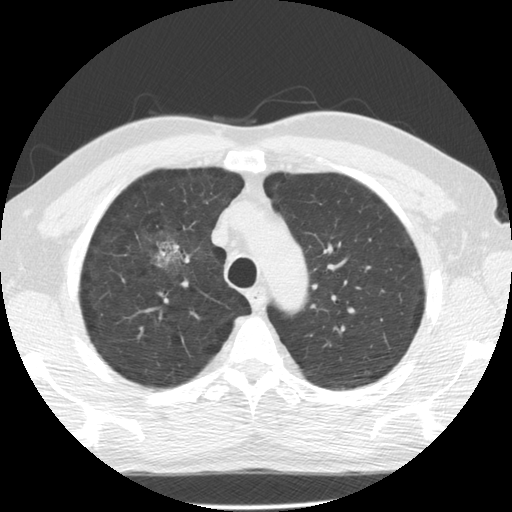
Low-dose screening chest CT, axial slice. Second annual screen. Lung window (W 1500 / L -600 HU). 2.5 mm slice thickness. Slice 100 of 135 in the series. 512 × 512 image matrix, field of view 350 × 350 mm. Male, age 60 years at enrolment.
Expert reader's lesion annotation, bounding box [x1, y1, x2, y2] px = [133, 221, 194, 281]. Screening reader's record for this exam (one nodule recorded; not confirmed to be the boxed lesion): non-calcified nodule or mass ≥4 mm, right upper lobe, poorly defined margins, mixed attenuation, pre-existing on the prior screen: yes; interval growth: yes. Lung cancer was diagnosed 562 days after this screen (after the third annual screen): papillary adenocarcinoma, NOS, right upper lobe, moderately differentiated (G2), stage IB (AJCC 6th edition), 32 mm at pathology.